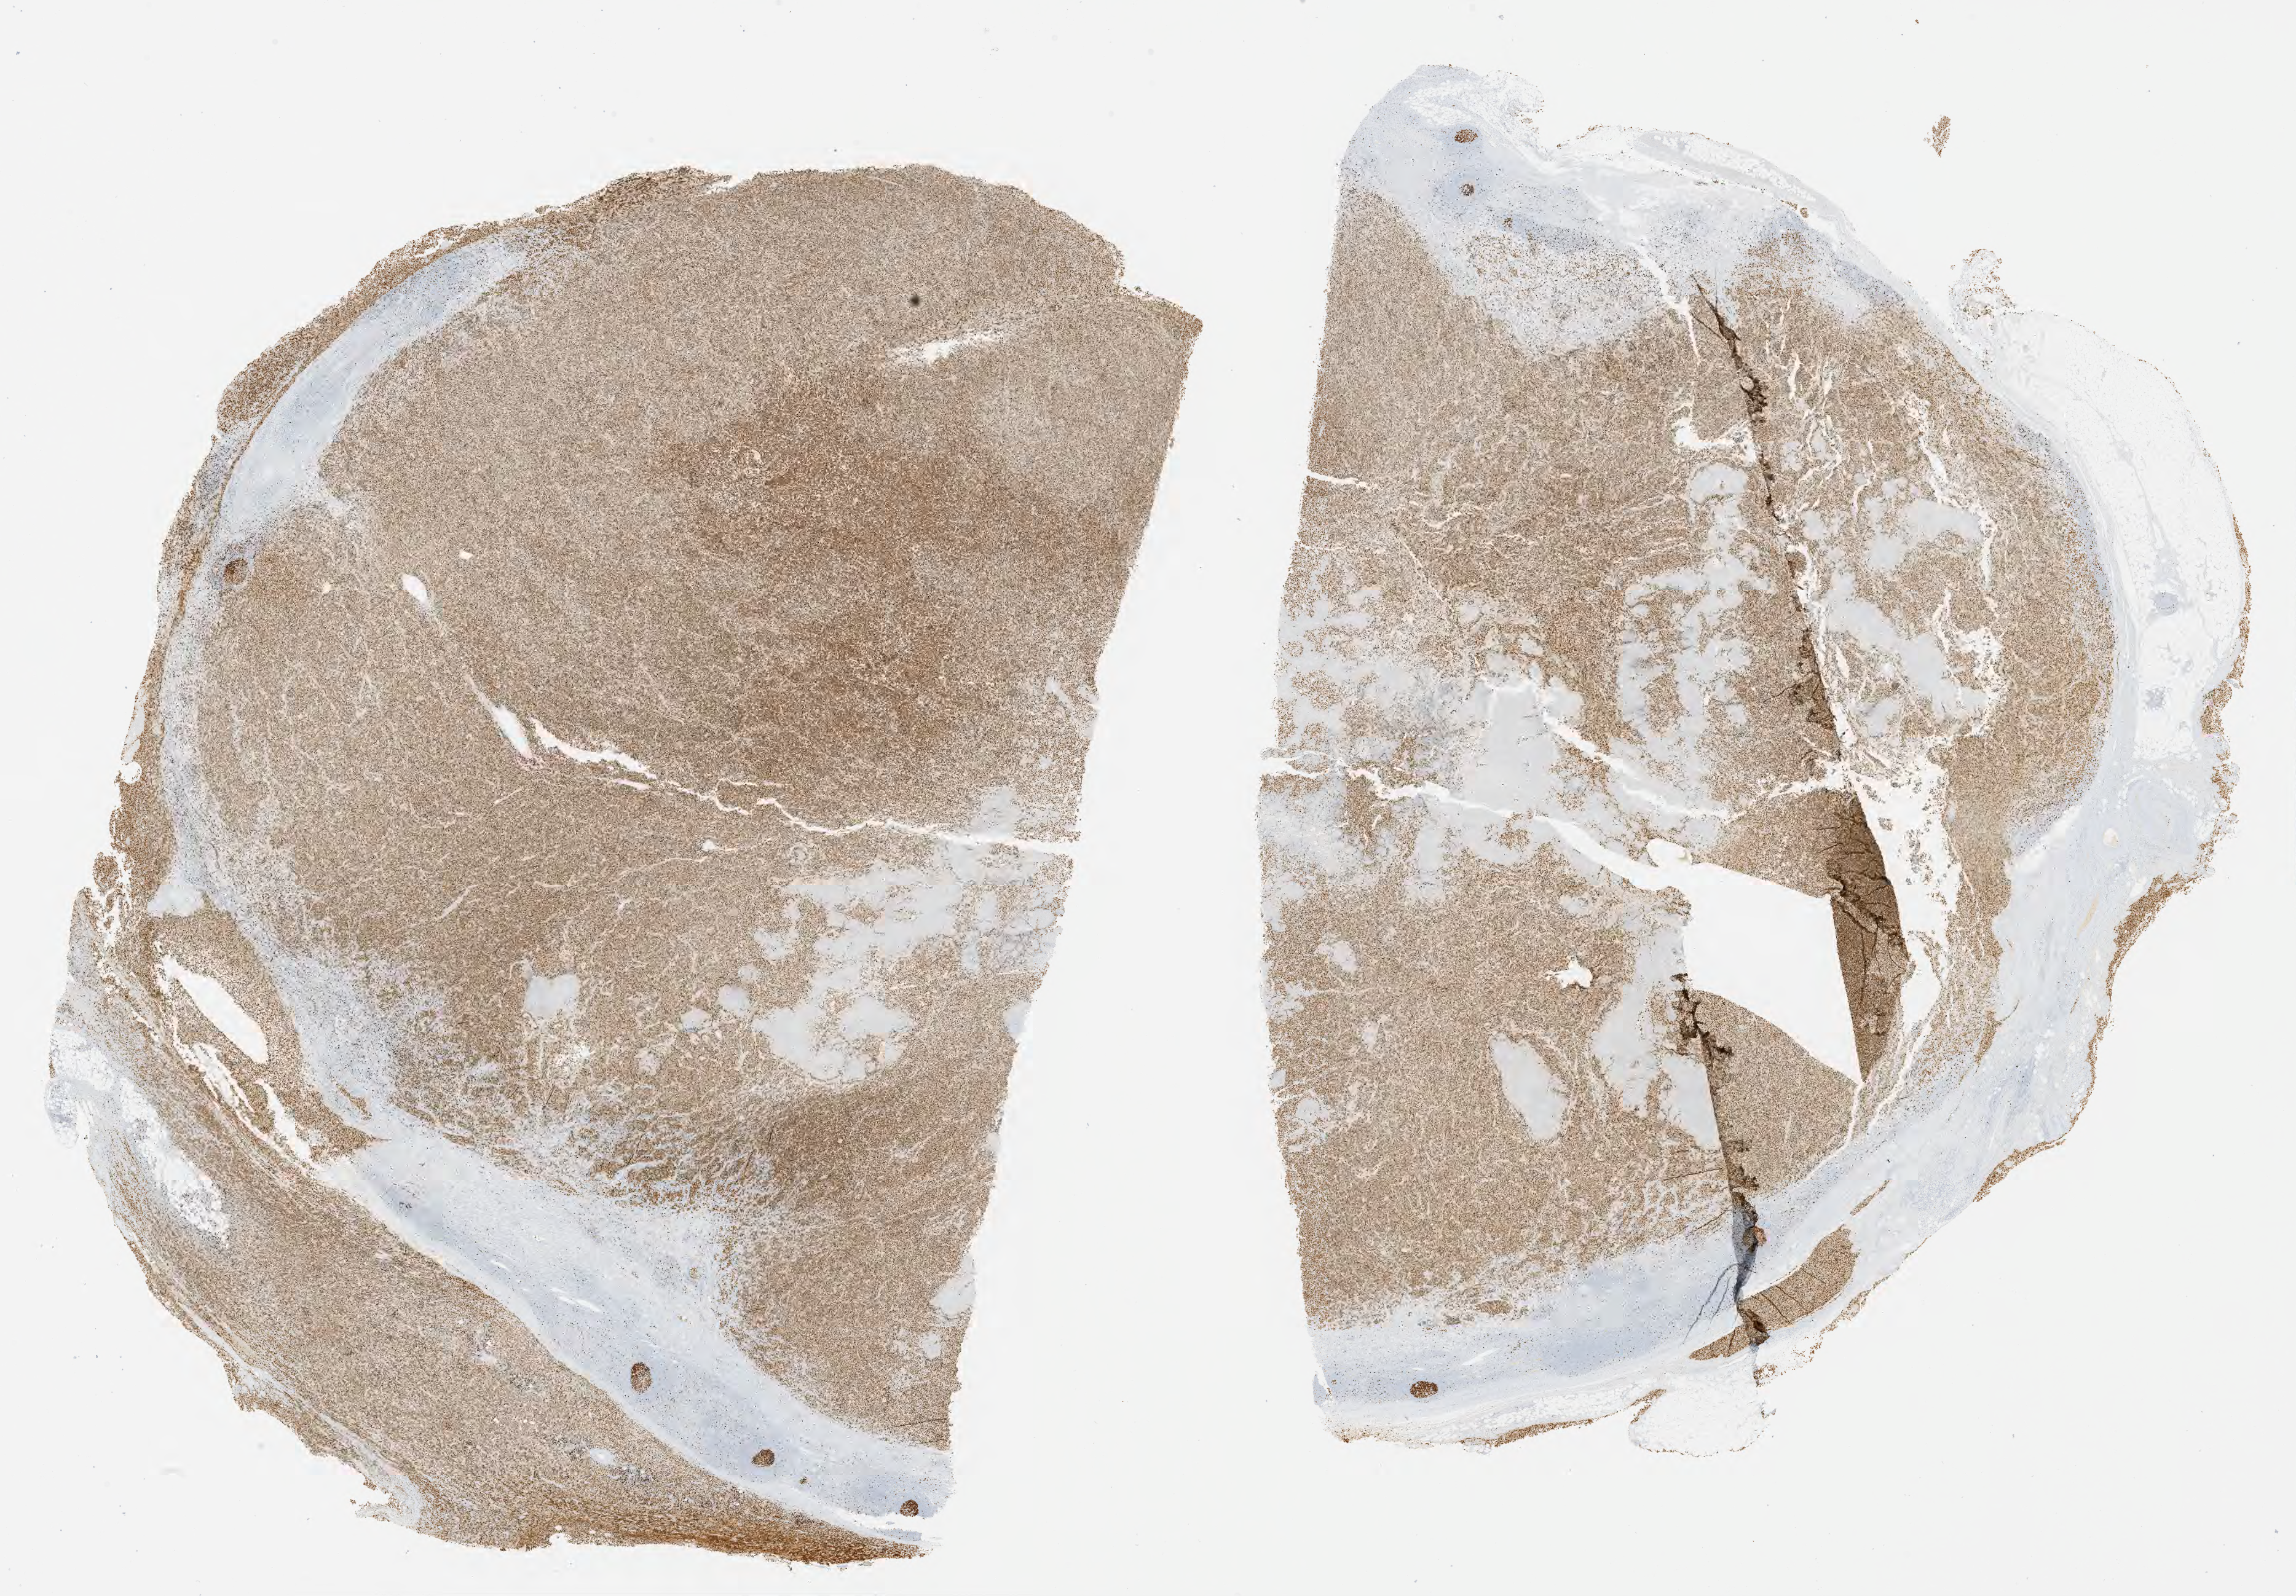
IHC for Ki-67, whole-slide image, low-resolution overview of the scanned area, about 30.2 x 21.0 mm; tumor tissue. Patient: male, age 48 years.
Histologic diagnosis: Burkitt lymphoma, NOS.